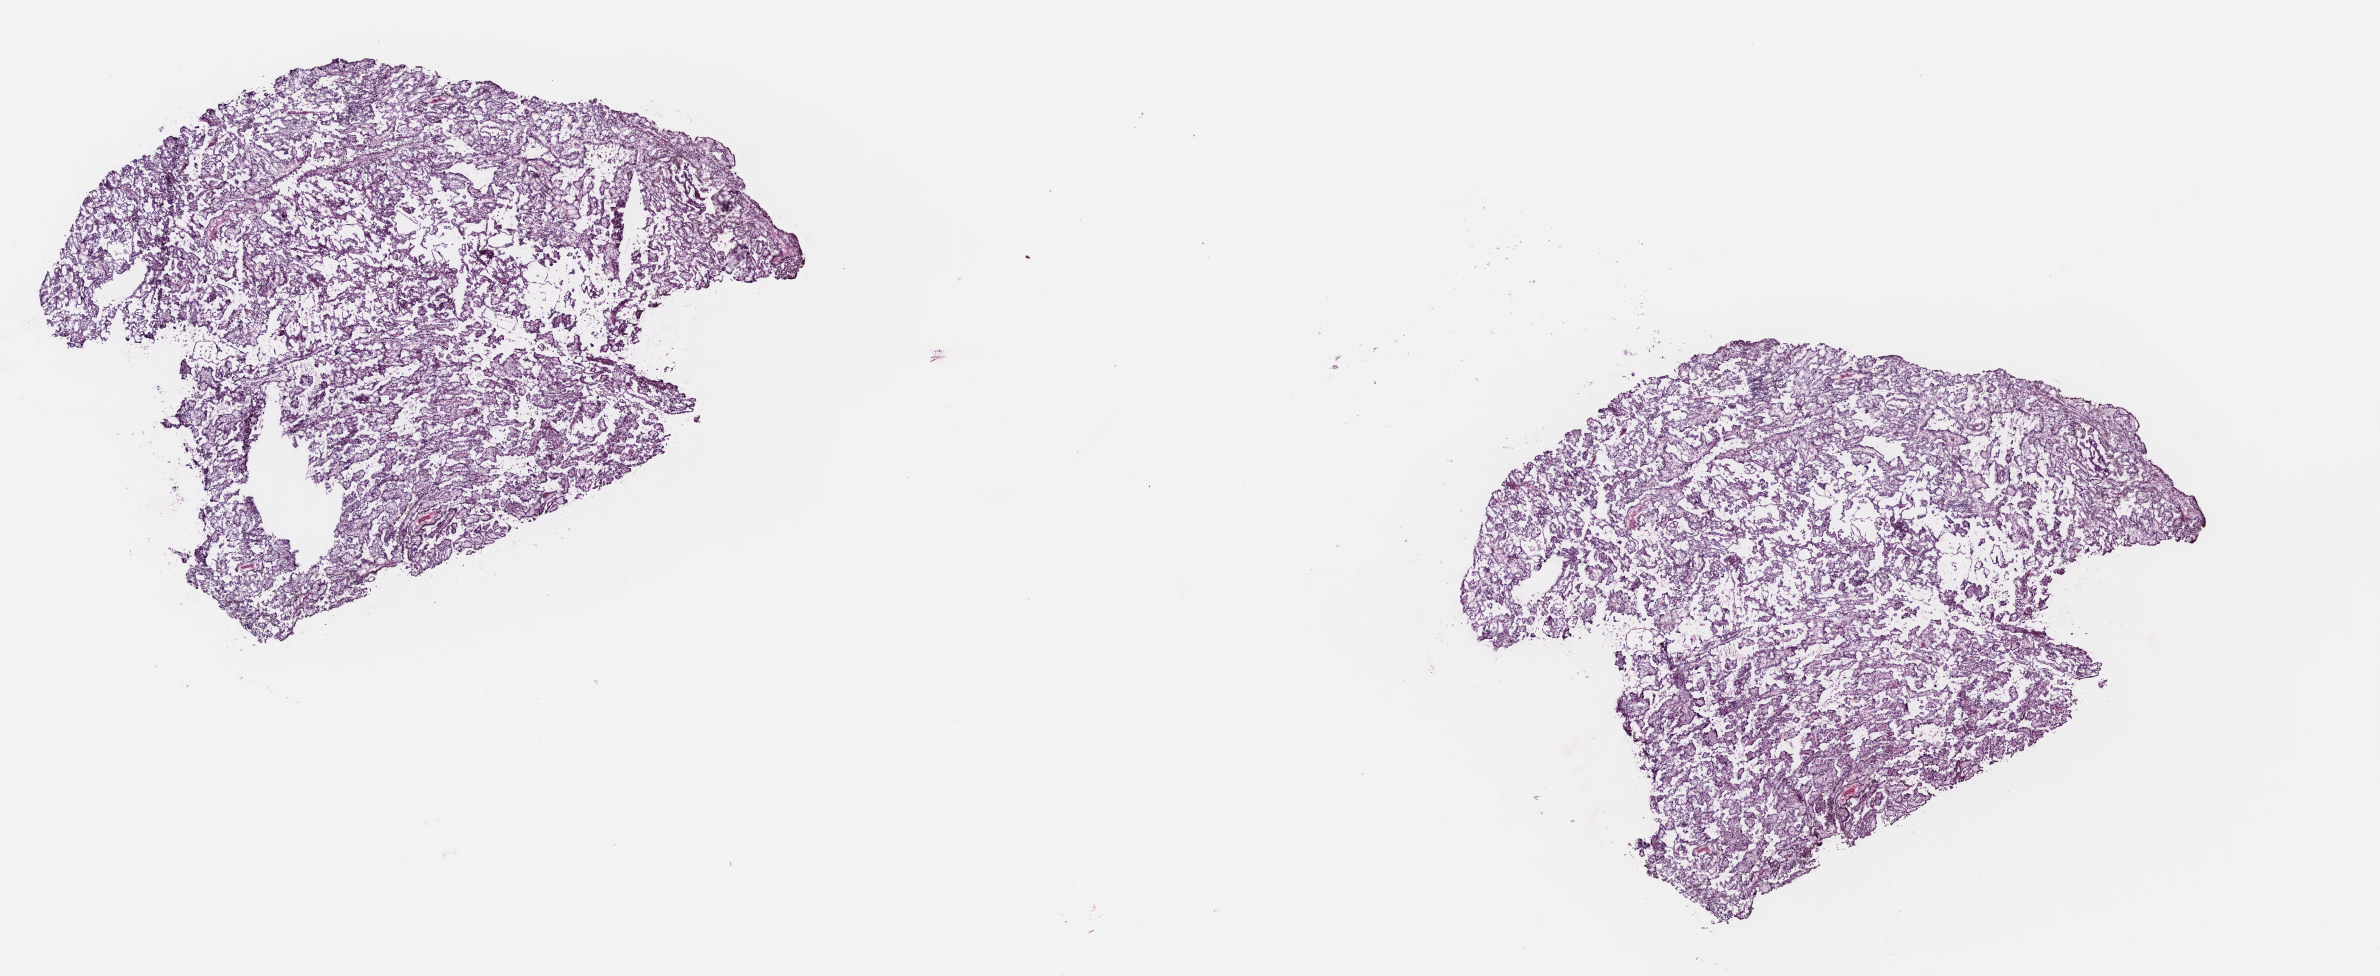
Digitized H&E tissue section (whole slide), low-resolution overview of the scanned area, about 18.7 x 7.7 mm (acquisition: 40x scan), frozen section, sample: primary tumour, kidney. Patient: male, age at initial diagnosis 57 years. Composition of this section per pathologist review: tumour cells 75%, tumour nuclei 75%, normal cells 0%, stromal cells 25%, necrosis 0%. Inflammatory infiltration, as recorded: lymphocyte infiltration 0%, monocyte infiltration 10%, neutrophil infiltration 0%.
* AJCC pathologic stage: I (7th edition)
* pathologic diagnosis: Papillary adenocarcinoma, NOS
* laterality: right